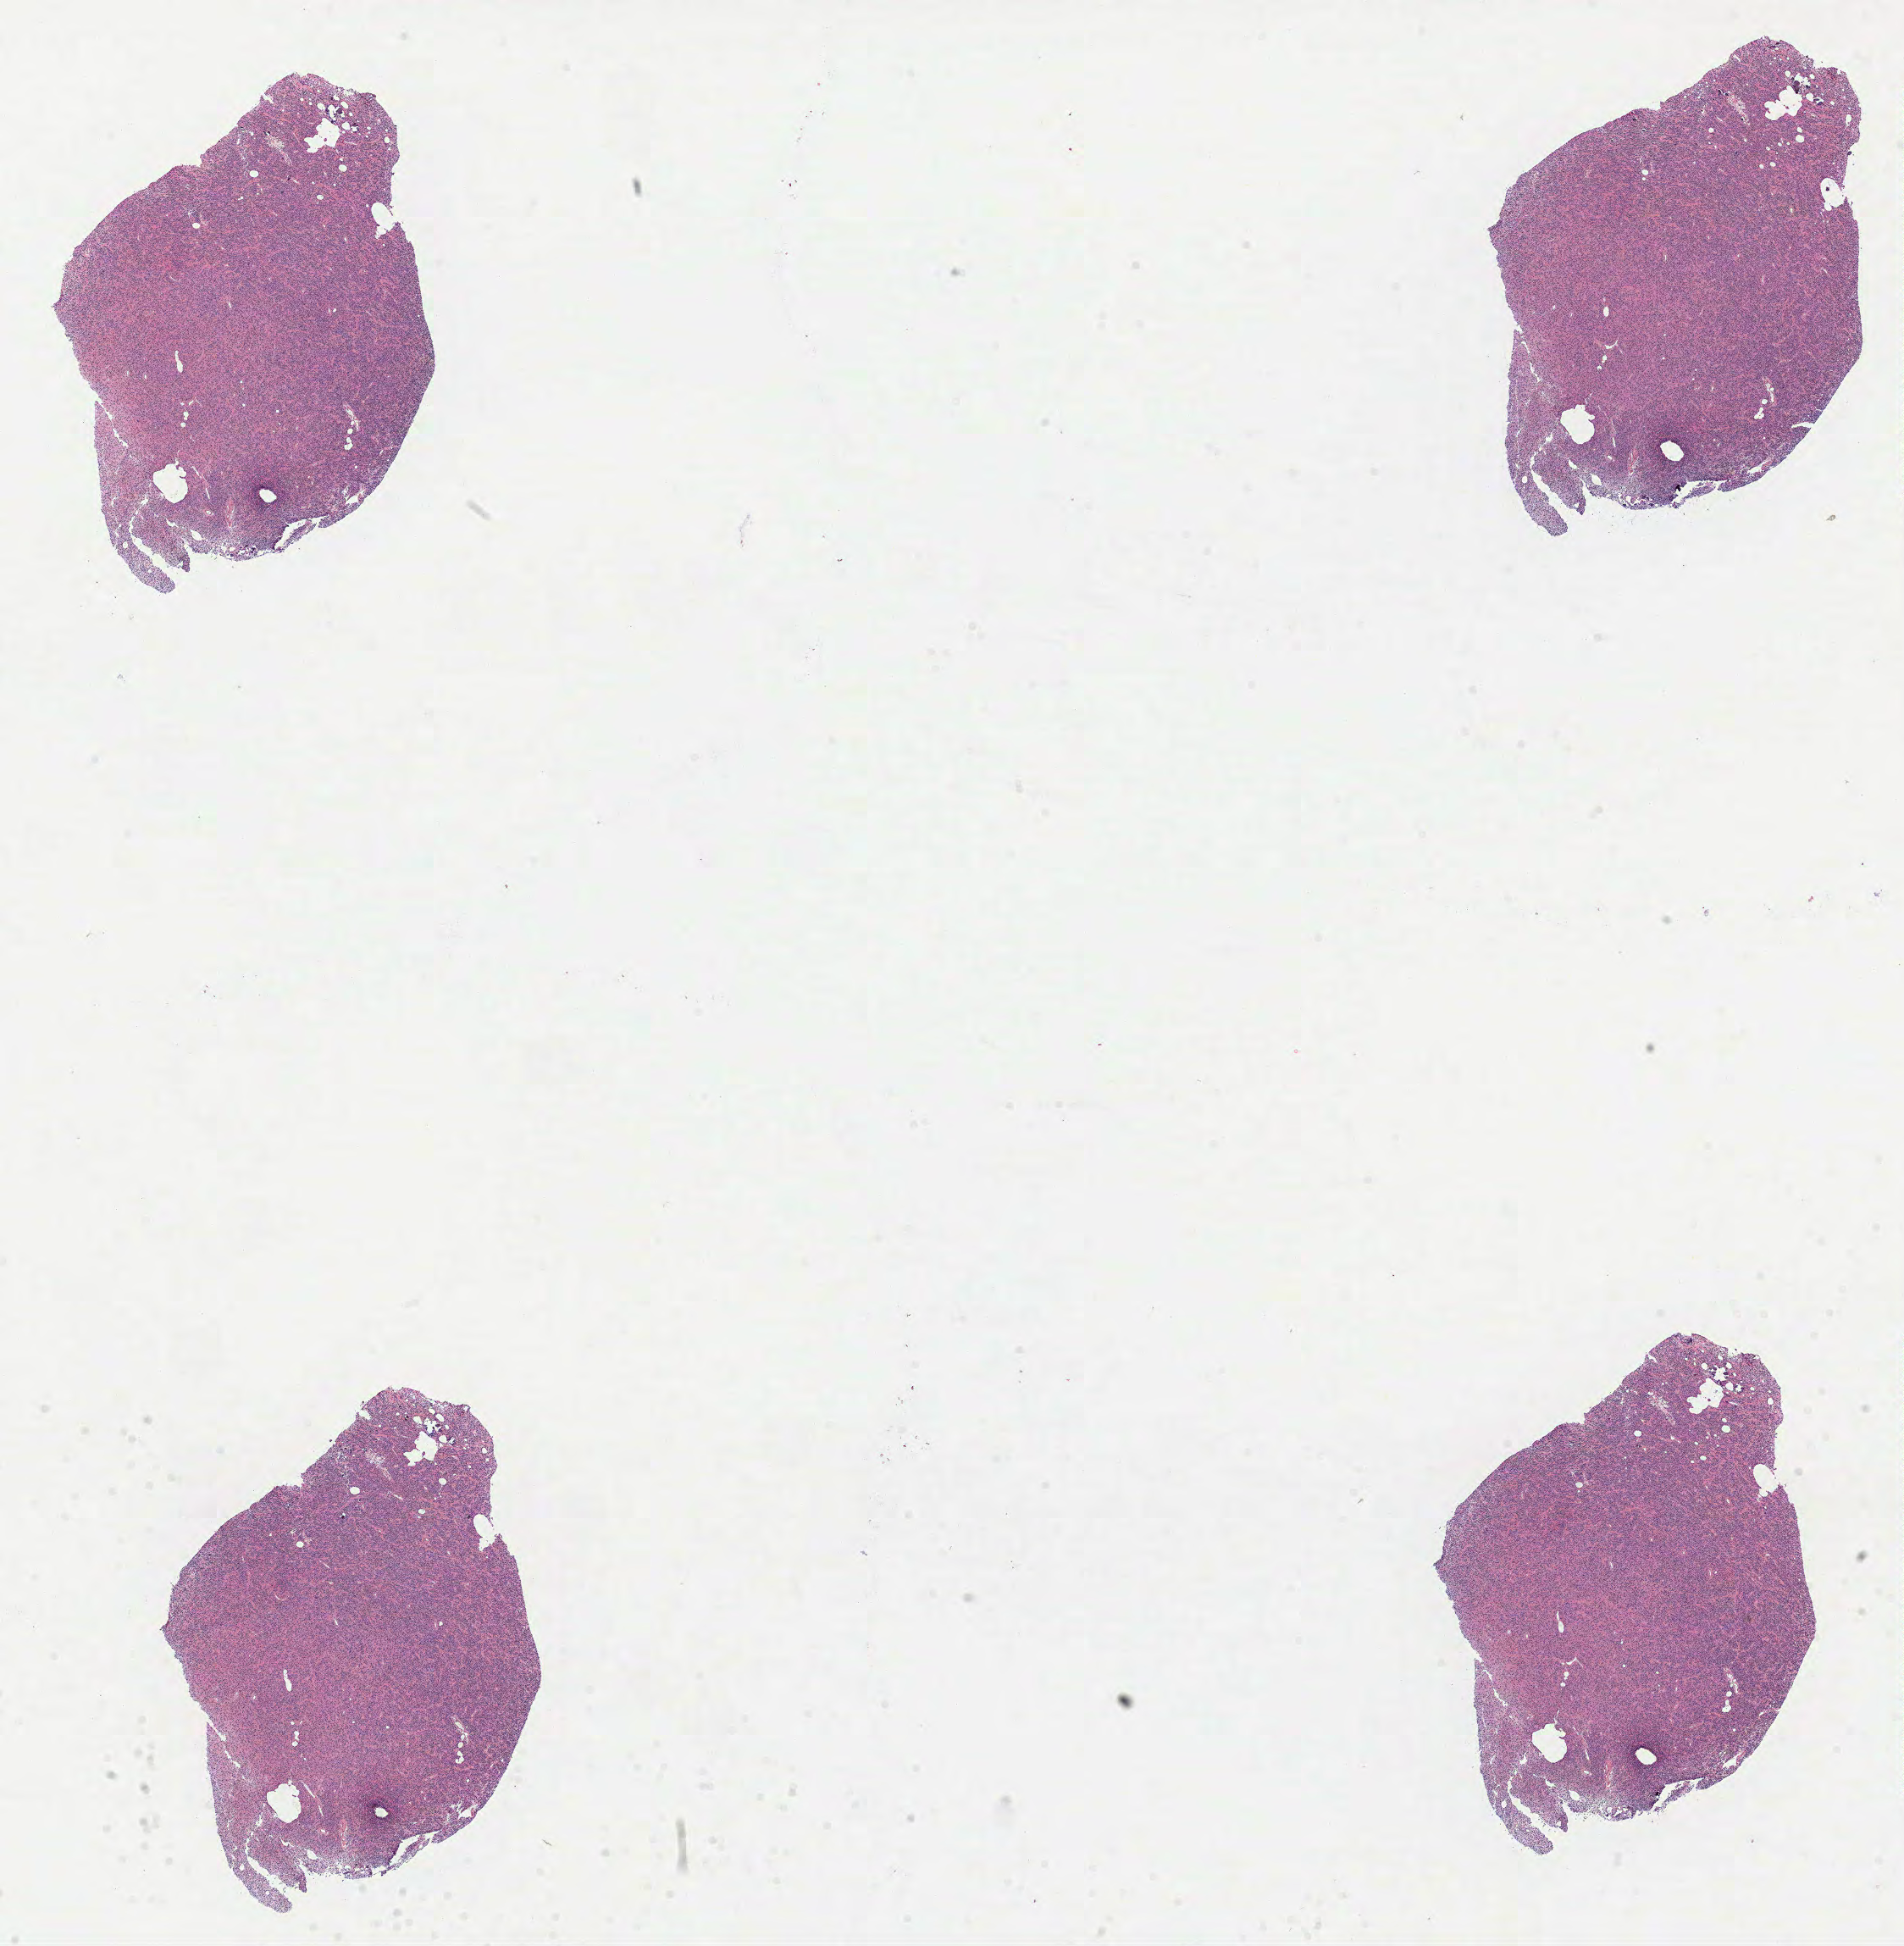
H&E whole-slide image — shown as a low-resolution overview of the whole scanned area (about 18.1 x 18.5 mm, from a 40x scan). Formalin-fixed paraffin-embedded (FFPE) diagnostic section. Primary tumour sample from the brain. Patient: male, age at initial diagnosis 53 years. Histologic grade: G3 (poorly differentiated).
- laterality: midline
- pathologic diagnosis: Oligodendroglioma, anaplastic (cerebrum)